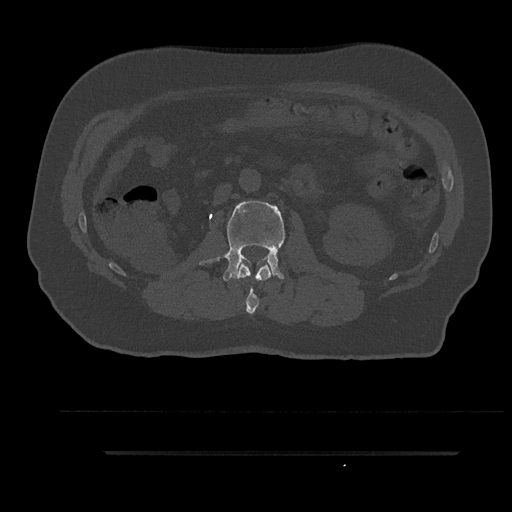
CT including the spine, one axial slice. Position 130 of 797 along the scan axis. Reconstruction kernel Br40s/3. 120 kVp. Bone window (W 1800 / L 400 HU). 512 × 512 image matrix. Male patient, age 63 years. From the clinical record (not read from this slice): primary cancer: renal; vertebrae with lytic lesions (as recorded): T8.
Annotated regions visible in this slice (semi-automatic segmentation, software-assisted and operator-edited):
- L1 vertebra: box from (x=234, y=262) to (x=272, y=314) px
- L2 vertebra: (x=199, y=201)–(x=286, y=281)